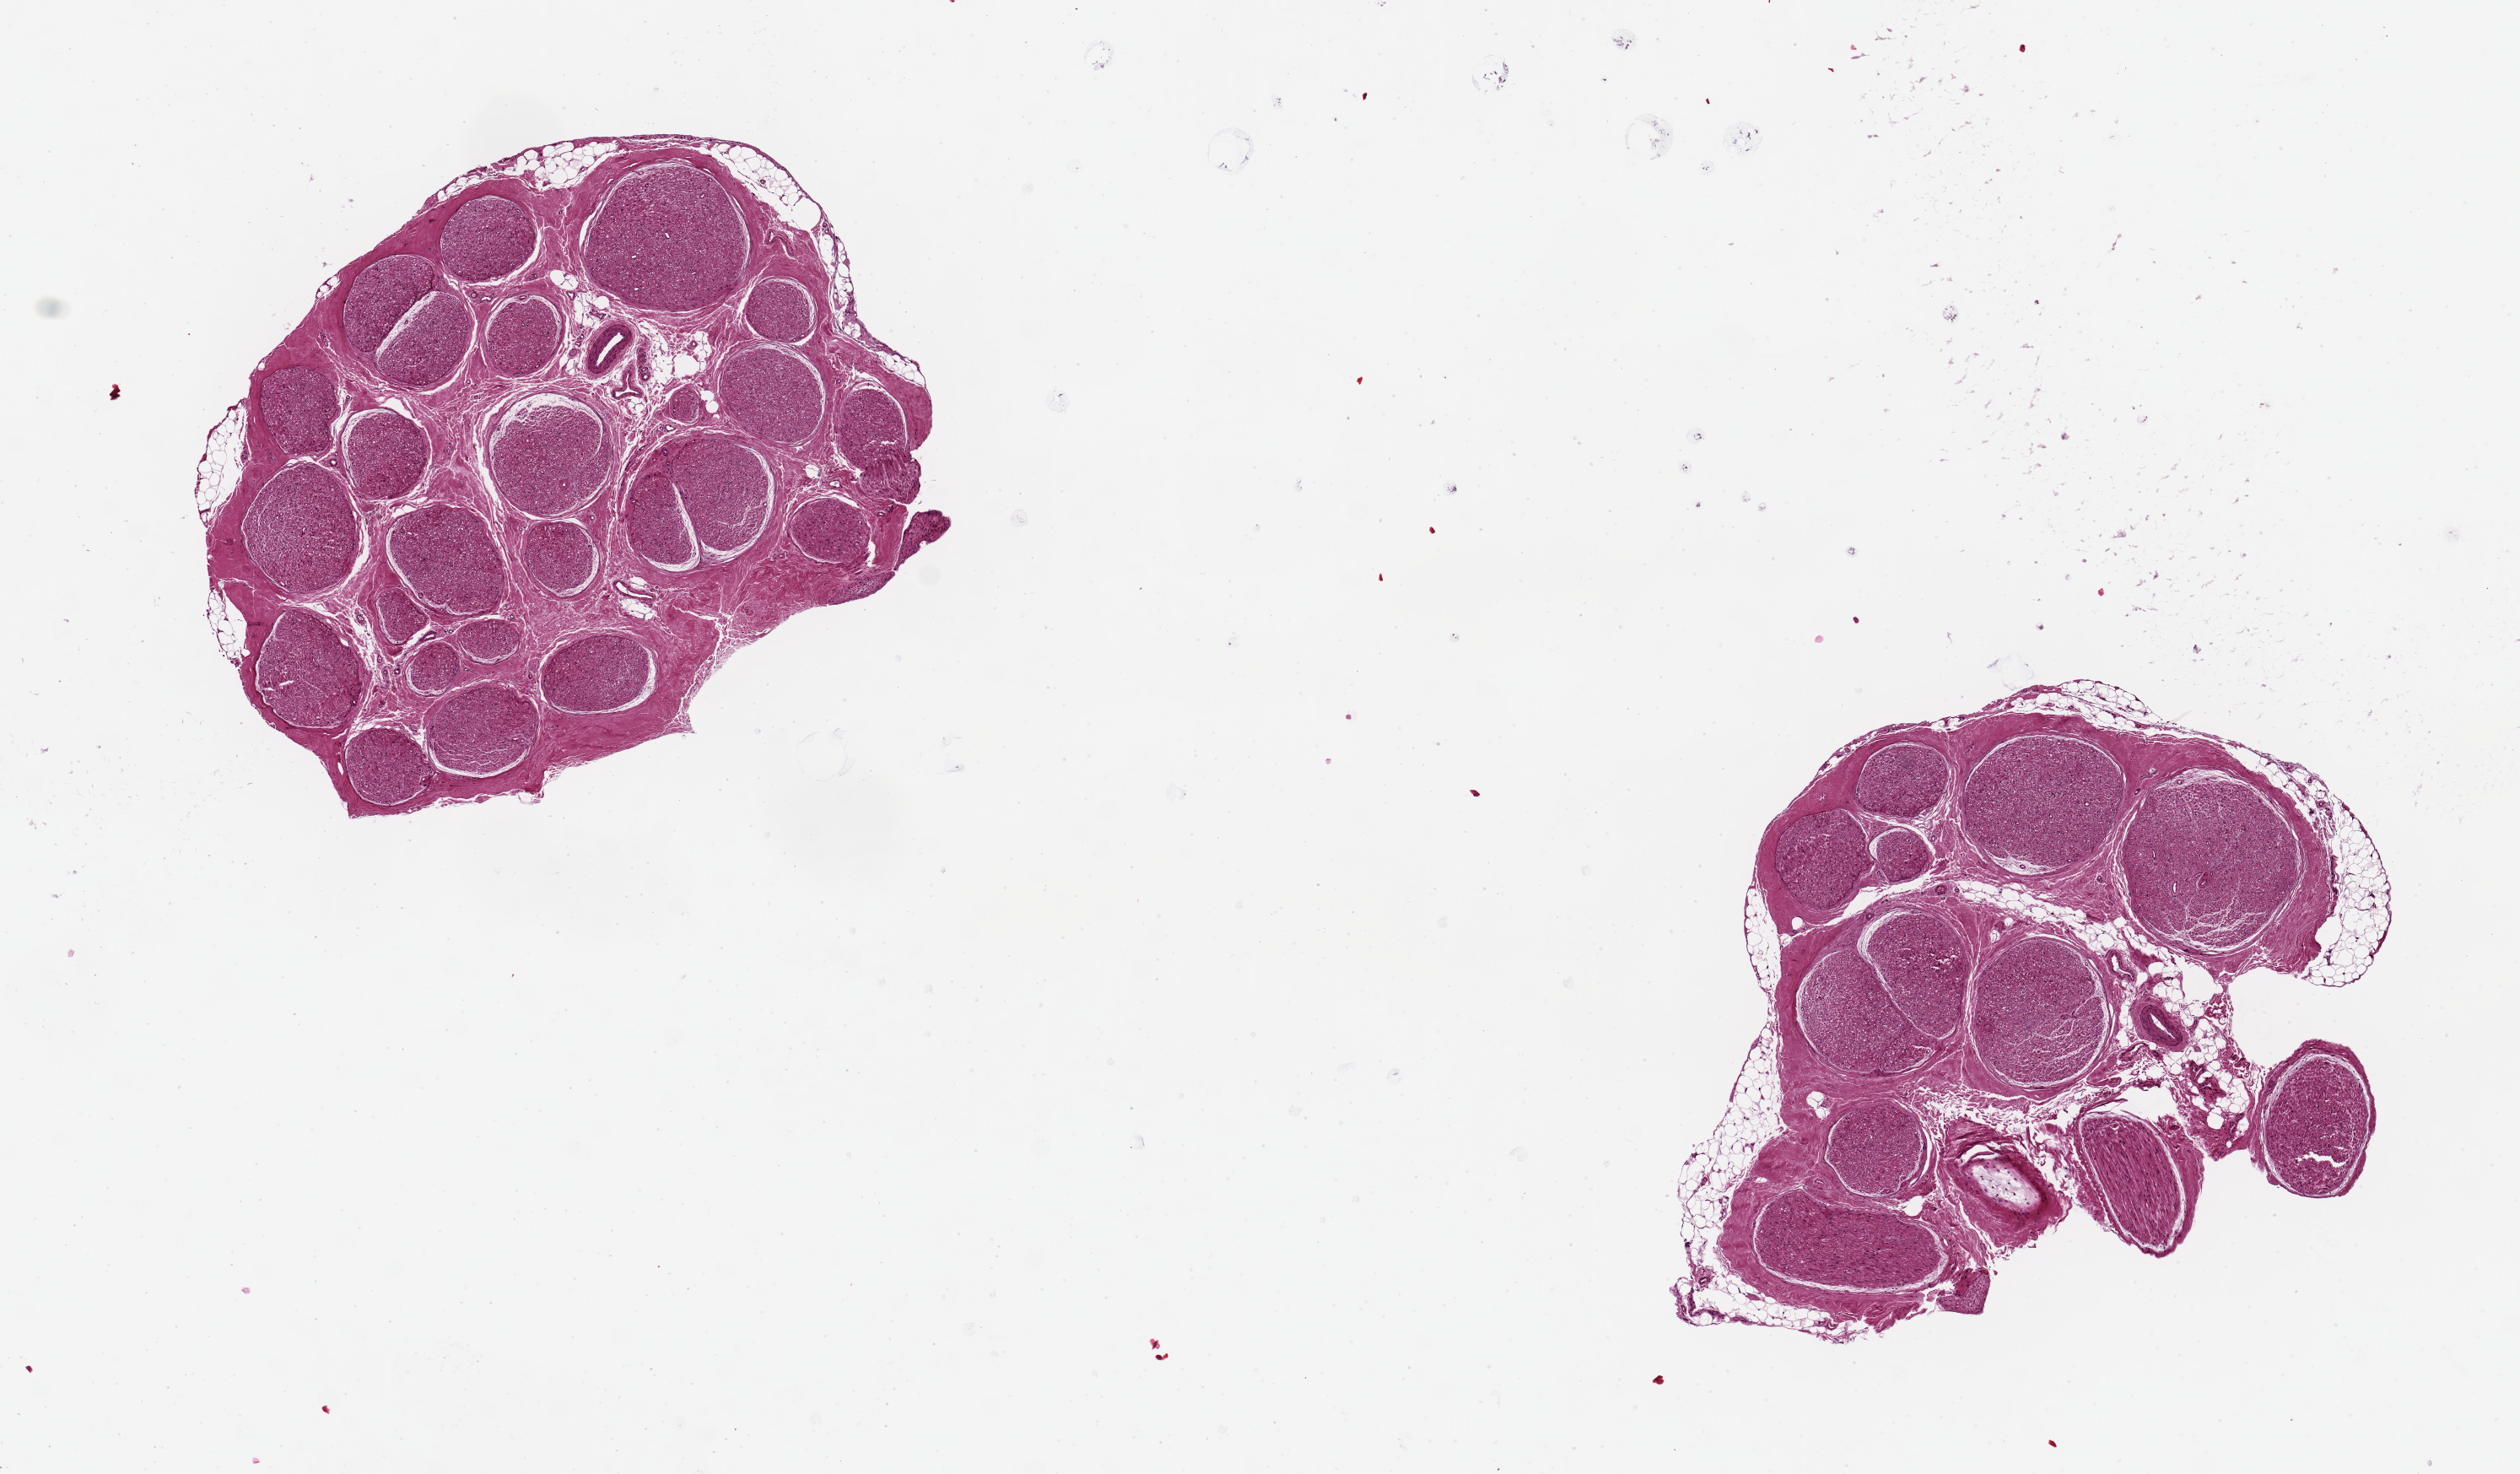
Whole-slide image, H&E stain — a low-resolution overview of the entire scanned area, about 11.8 x 6.9 mm (from a 20x scan); PAXgene-fixed paraffin-embedded (PFPE) section; section of tibial nerve (target tissue); donor tissue sample.
Review note (as recorded): 2 aliquots. Good clean specimen, minimal adherent fat.